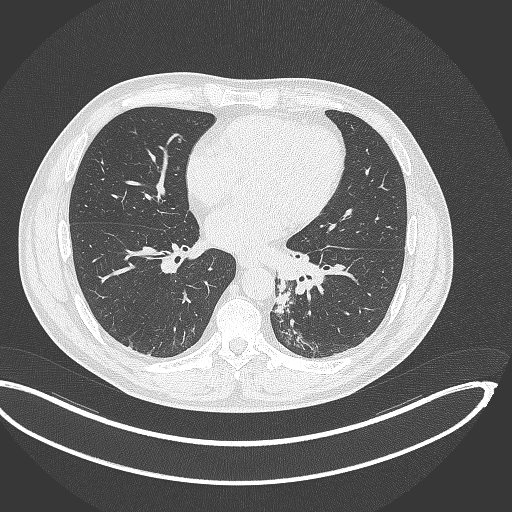
Chest CT, one axial slice. Position 150 of 362 along the scan axis. Reconstruction kernel B70f. 120 kVp. Lung window (W 1500 / L -600 HU). 1 mm slice thickness. 512 × 512 image matrix. Patient: male, 50 years. Case-level facts recorded for this patient, not image findings: clinical TNM (as recorded): T2a N3 M0.
Structures marked on this image (rectangle marked by the reading radiologist):
- lung tumour (recorded histology: squamous cell carcinoma): bounding box [x1, y1, x2, y2] px = [269, 280, 289, 316]